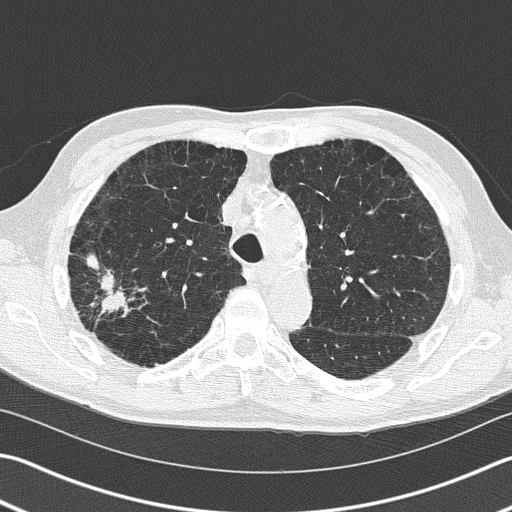
Low-dose screening chest CT, axial slice; first (baseline) screen; lung window (W 1500 / L -600 HU); 2 mm slice thickness; 120 kVp; slice 52 of 163 in the series. Male, age 66 years at enrolment. Current smoker at enrolment.
• Expert-annotated lung lesion, bounding box [x1, y1, x2, y2] px = [62, 242, 136, 338].
• The exam's reader record, not a measurement of the box and not confirmed to be the same lesion: non-calcified nodule or mass ≥4 mm, right upper lobe, 39 × 23 mm, spiculated (stellate) margins, soft tissue attenuation.
• Official screen result: positive, change unspecified: nodule(s) >= 4 mm or enlarging nodule(s), mass(es), or other non-specific abnormalities suspicious for lung cancer.
• Lung cancer was diagnosed 36 days after this screen: squamous cell carcinoma, NOS, right upper lobe, poorly differentiated (G3), stage IB (AJCC 6th edition), 23 mm at pathology.